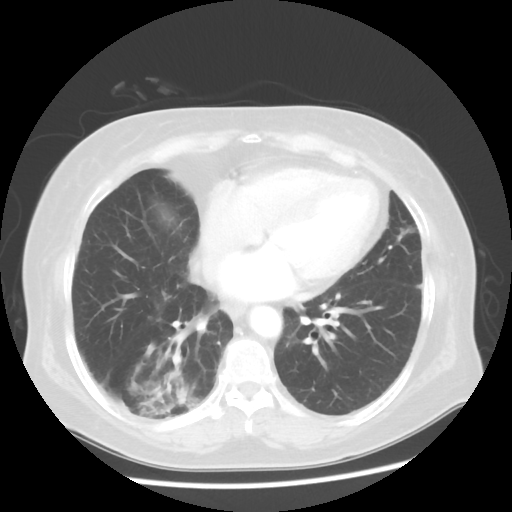
Chest CT, one axial slice; position 21 of 56 along the scan axis; 120 kVp; lung window (W 1500 / L -600 HU); 512 × 512 image matrix, field of view 360 × 360 mm. Patient: female, 64 years. Case-level facts recorded for this patient, not image findings: clinical TNM (as recorded): Tis N0 M0.
Annotated regions visible in this slice (bounding box drawn by a radiologist):
- lung tumour (recorded histology: adenocarcinoma): bounding box <124,363,196,424> (left, top, right, bottom; pixels)